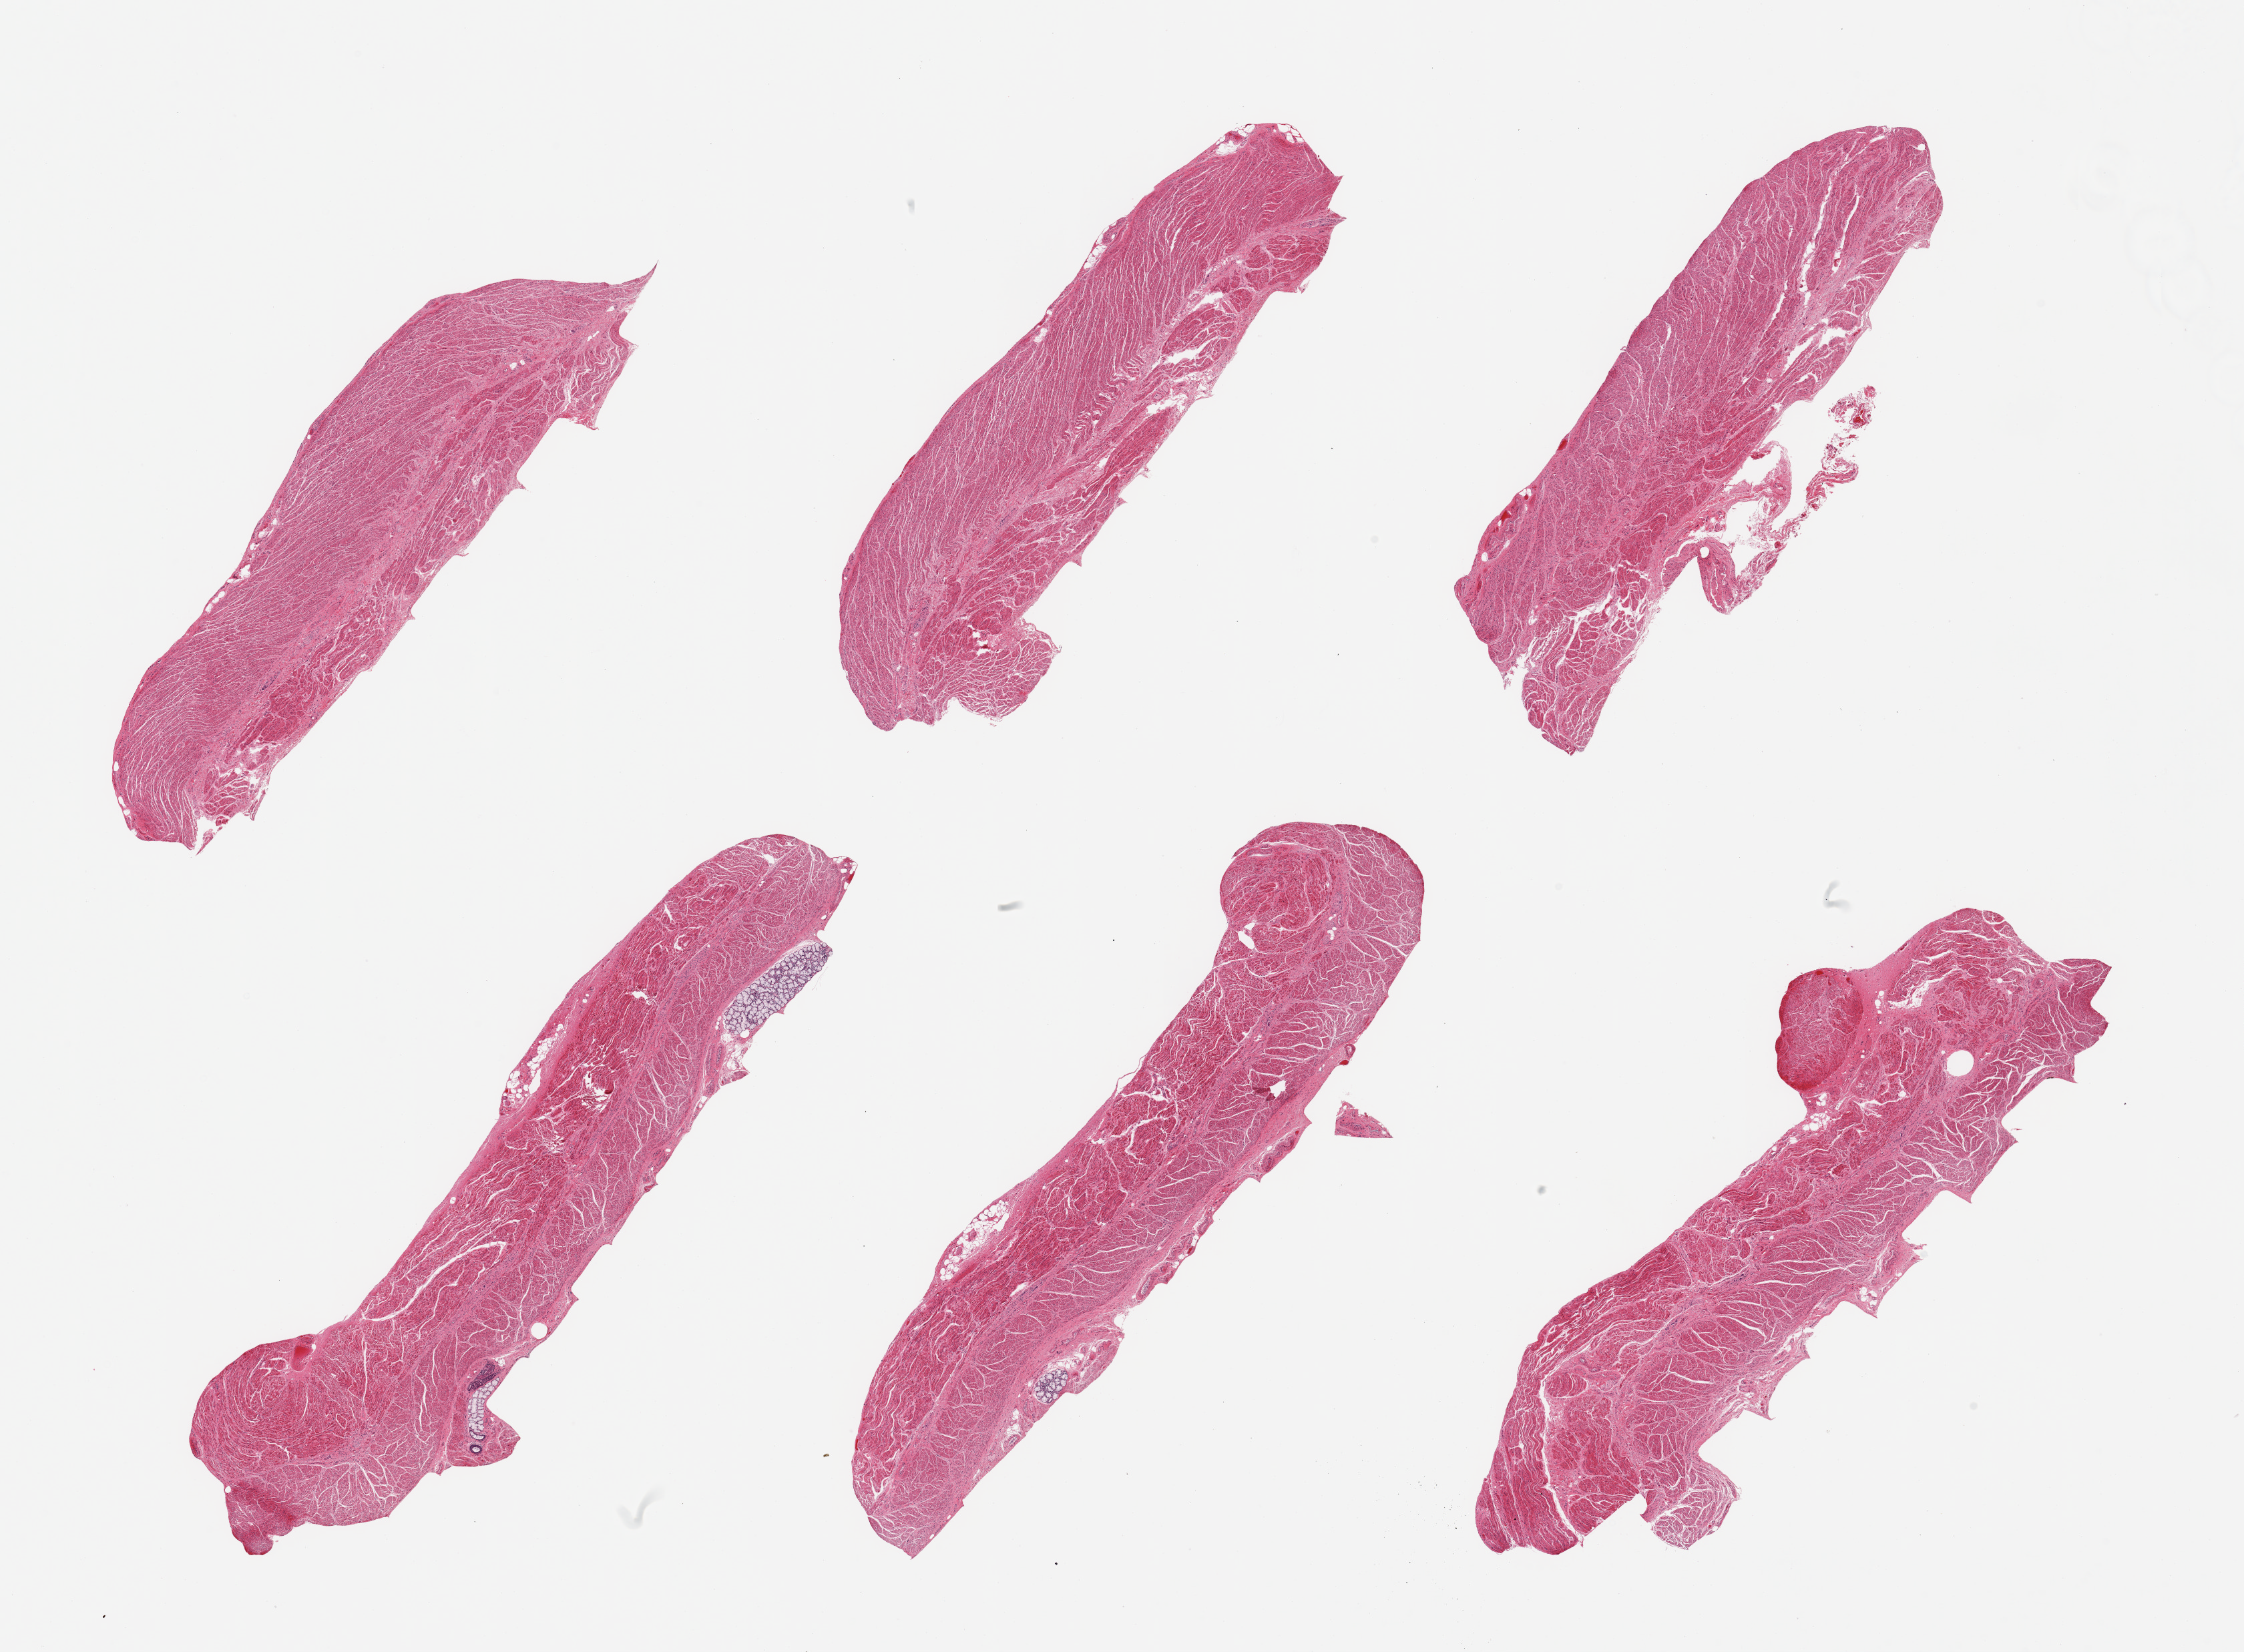
Haematoxylin and eosin whole-slide image, brightfield, shown as a low-resolution overview of the whole scanned area (about 26.6 x 19.6 mm, from a 20x scan), PAXgene-fixed, paraffin-embedded tissue, section of gastroesophageal junction (target tissue), donor tissue sample. Female donor.
Review note (as recorded): 6 pieces; well trimmed muscle except for 1.4mm submucosal gland on 1.